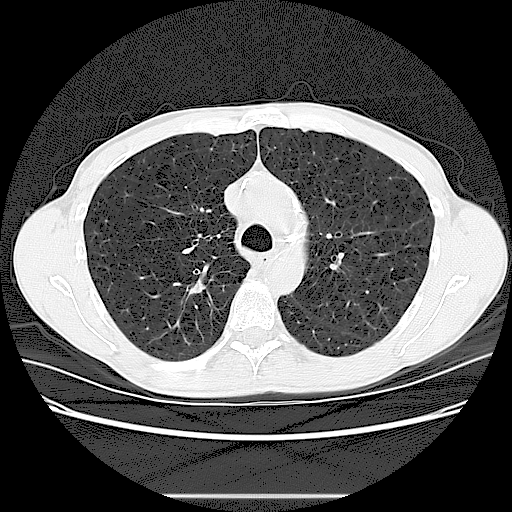
Low-dose screening chest CT, one axial slice. Reconstruction kernel LUNG. Lung window (W 1500 / L -600 HU). 2.5 mm slice thickness. 512 × 512 image matrix, field of view 360 × 360 mm.
Outlined on this slice (outlined manually by an expert reader):
- lesion 1 (tumor, upper lobe of right lung): bounding box [x1, y1, x2, y2] px = [190, 279, 205, 294]